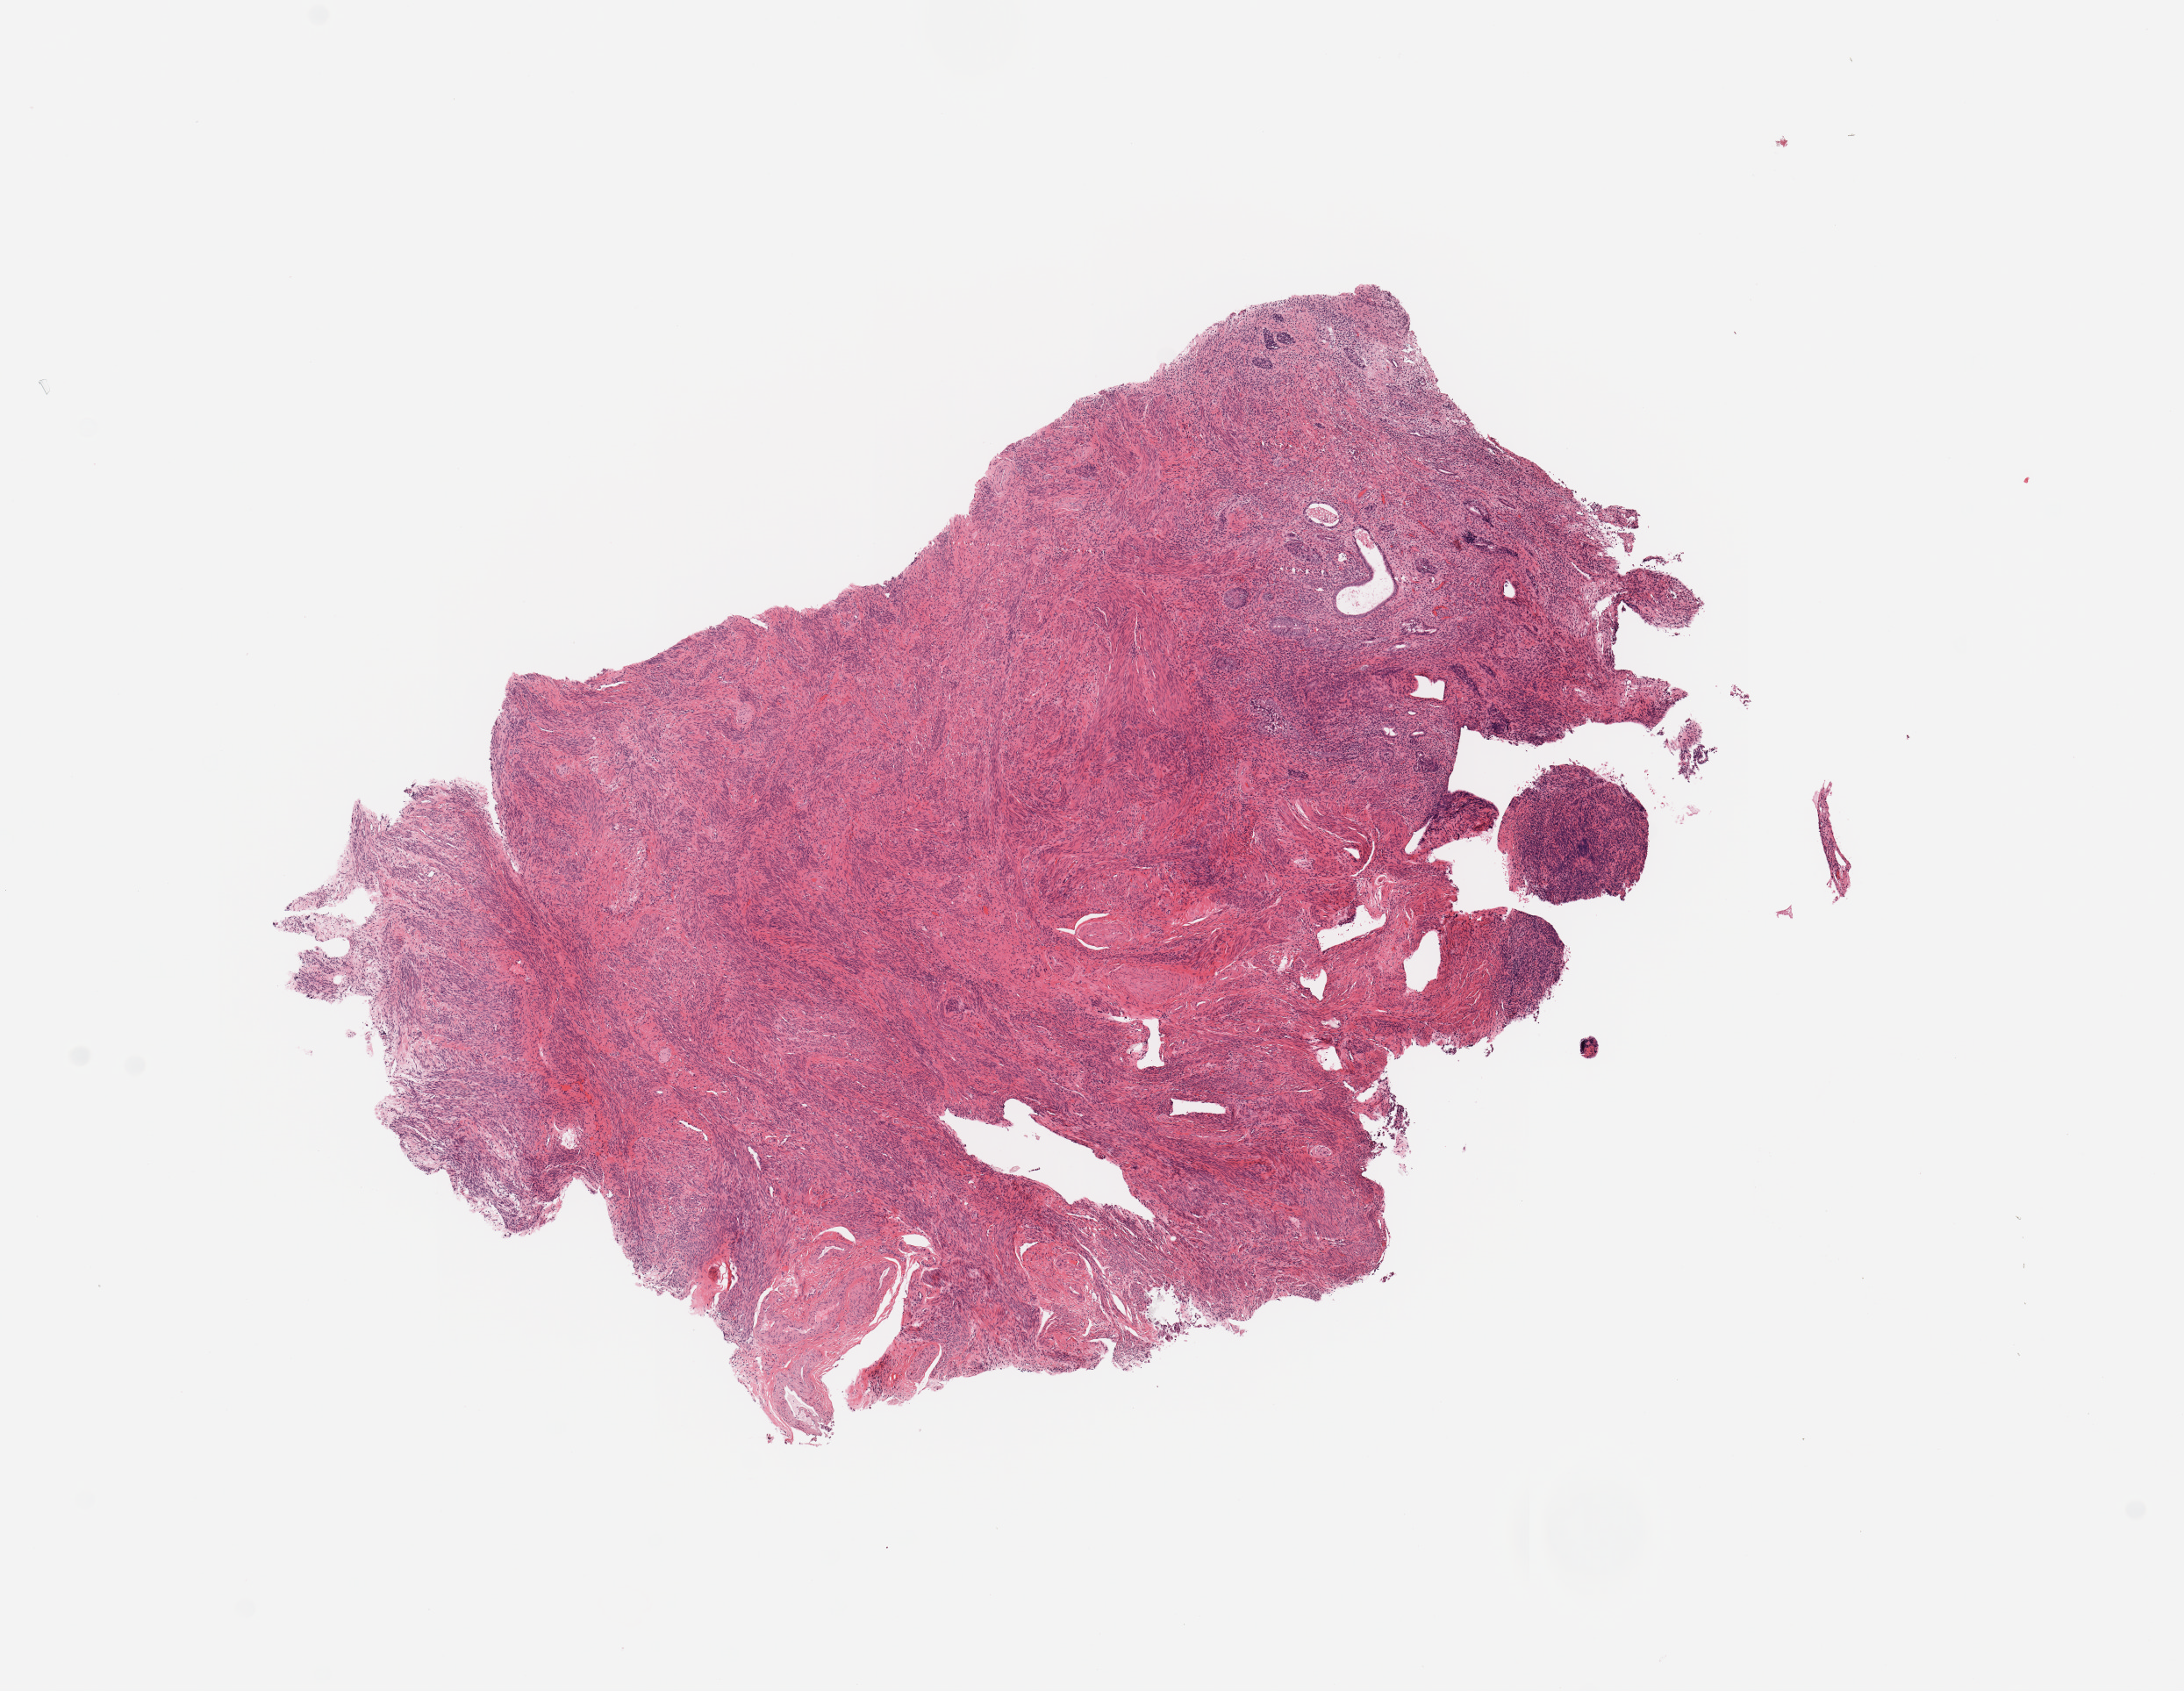
Hematoxylin and eosin (H&E) stained whole-slide image — low-resolution overview of the scanned area, about 9.8 x 7.6 mm (slide scanned at 20x). Uterus, normal (non-tumour) tissue. 59-year-old female patient.
• this section: normal (non-tumour) tissue from the same patient
• patient diagnosis: Endometrioid adenocarcinoma, NOS